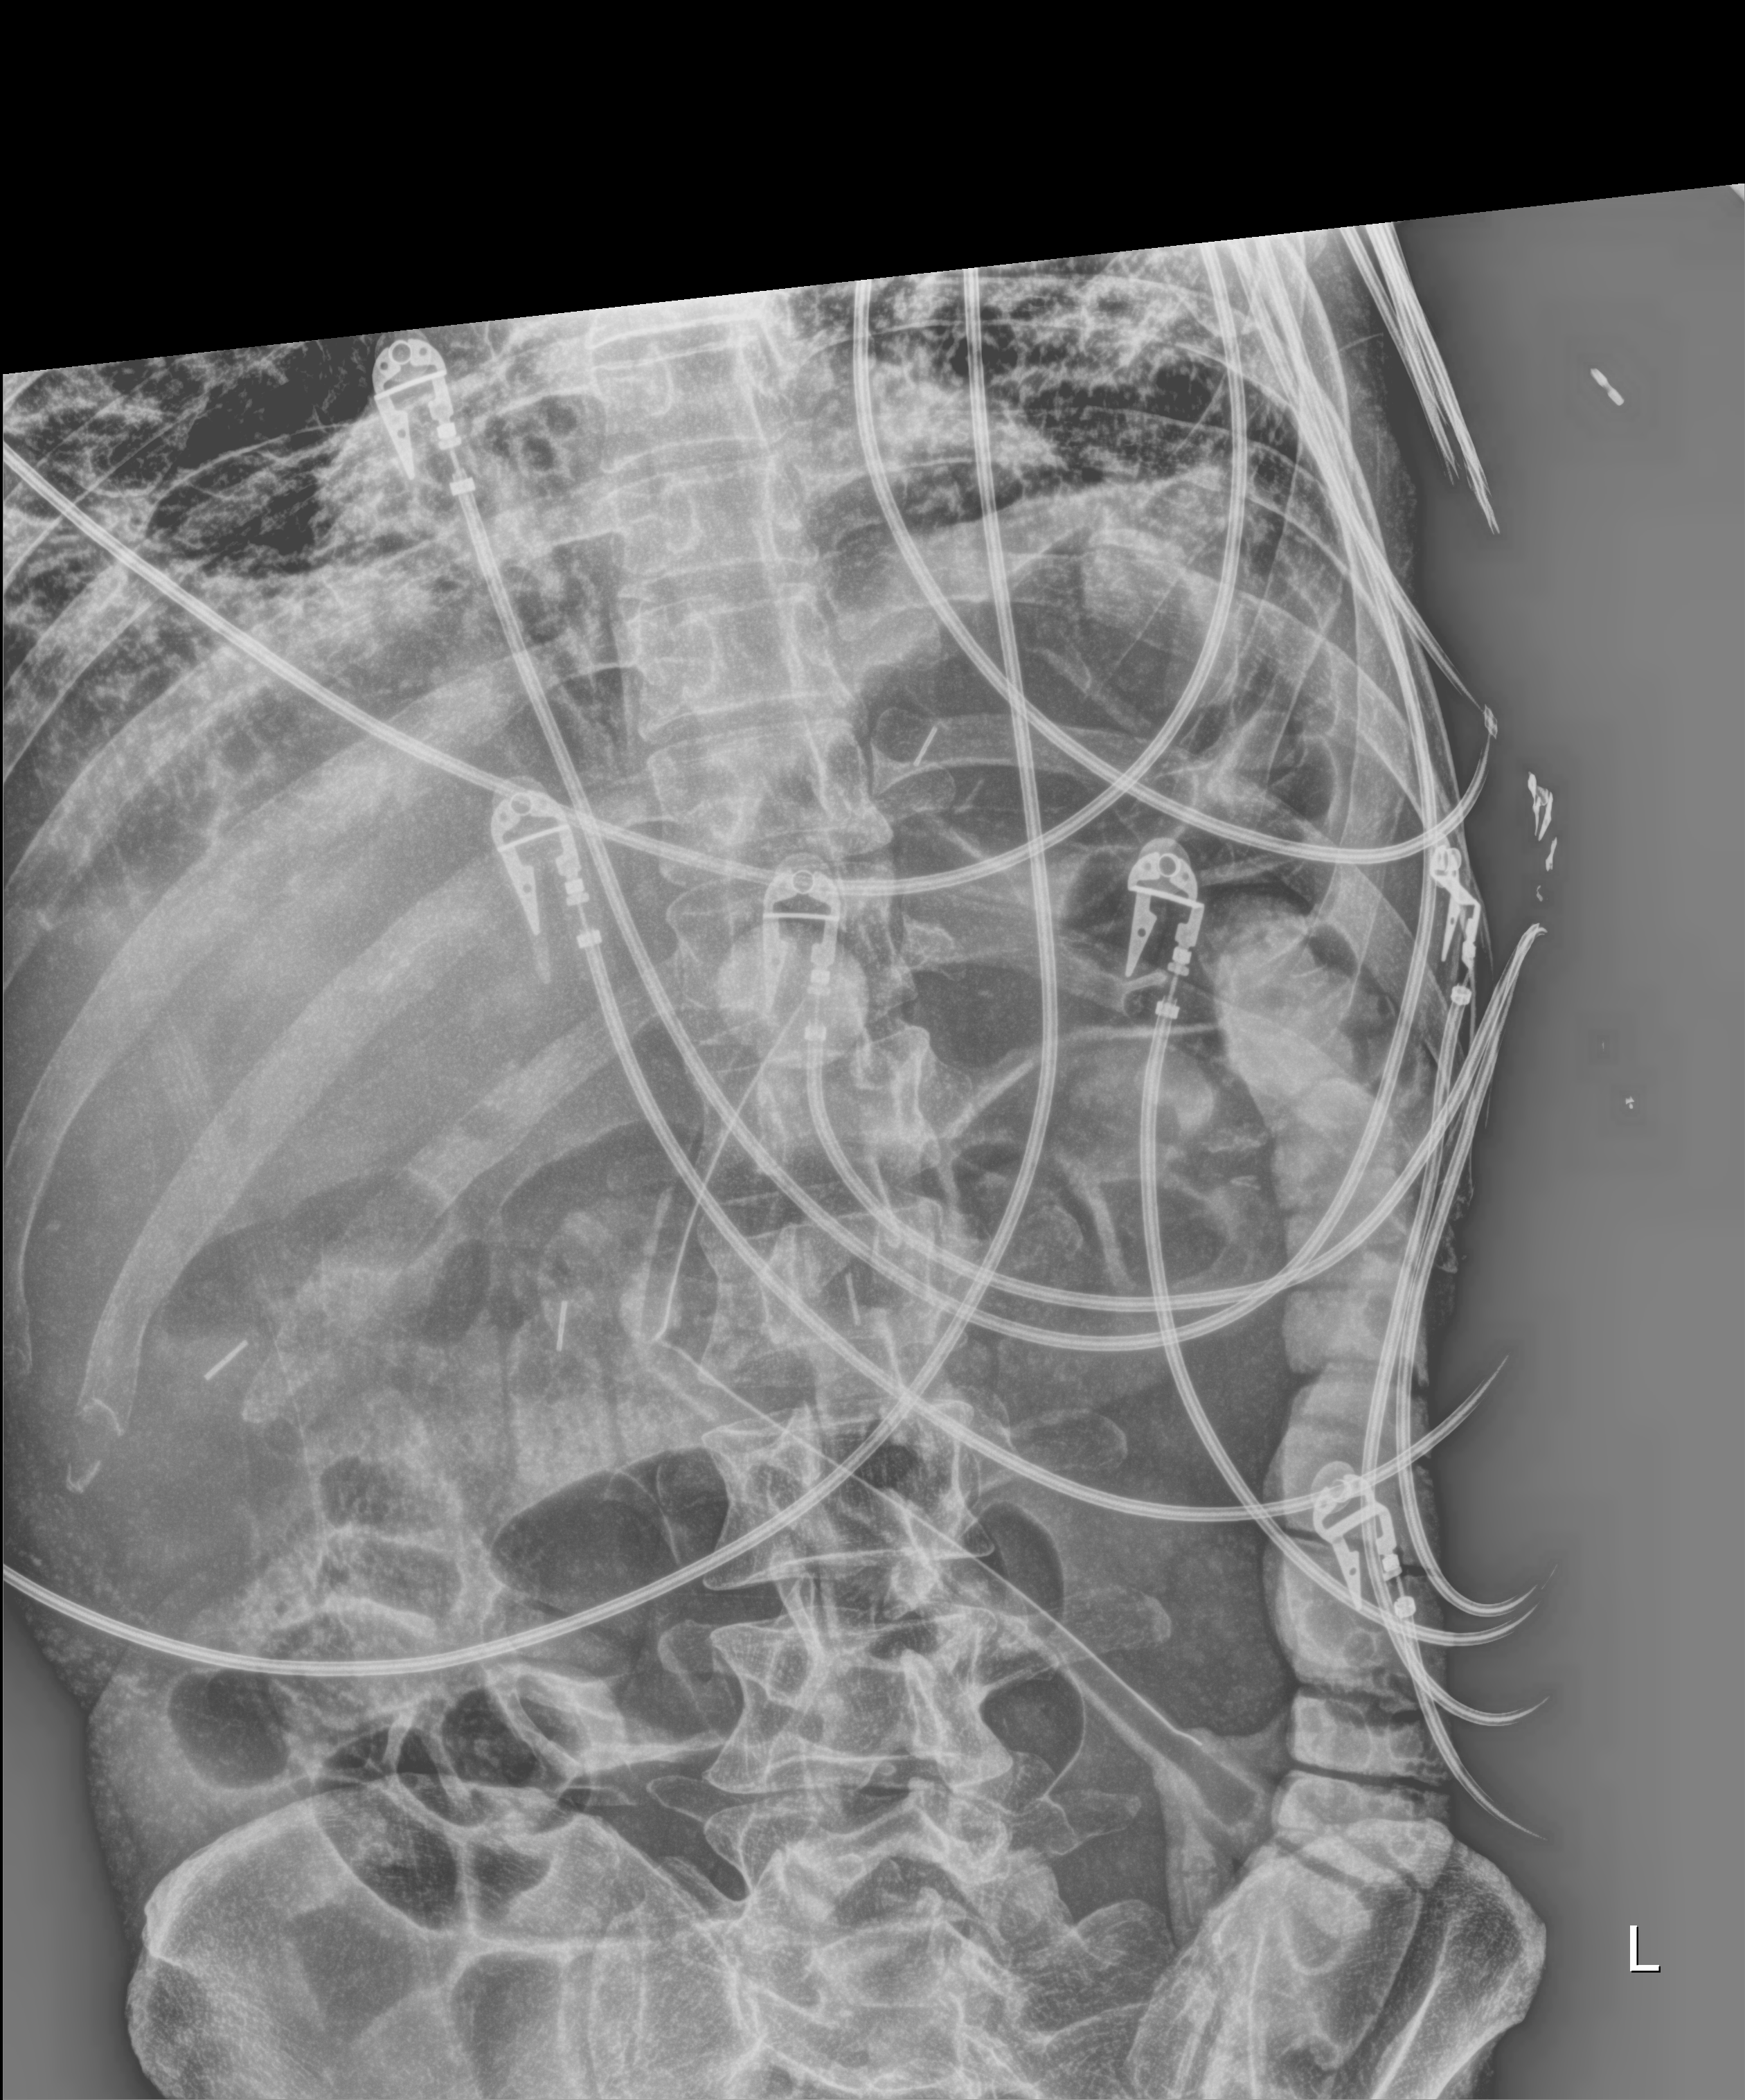
Bedside abdomen radiograph (digital radiography); anteroposterior (AP) projection. Male patient hospitalised with COVID-19, age 18–59 years.
Admission-level facts for this patient (not findings on this image; timing relative to this image not recorded): admitted to intensive care during this hospital stay: yes.